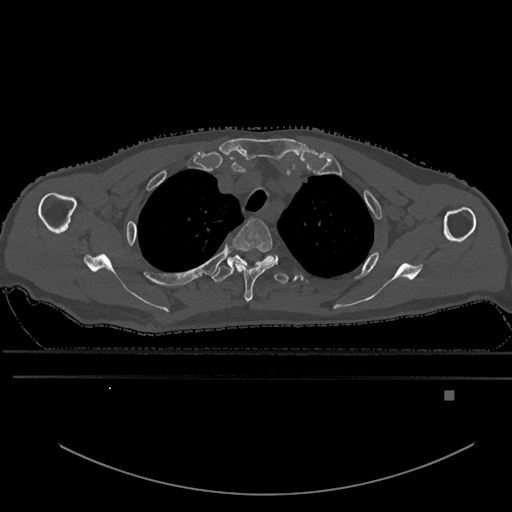
CT including the spine, one axial slice. Position 479 of 969 along the scan axis. Bone window (W 1800 / L 400 HU). 512 × 512 image matrix, field of view 456 × 456 mm. Patient: male, 82 years. Case-level facts recorded for this patient, not image findings: primary cancer: prostate.
Annotated regions visible in this slice (semi-automatically segmented with operator editing):
- T2 vertebra: bounding box <232,218,279,302> (left, top, right, bottom; pixels)
- T3 vertebra: <212,254,288,285>